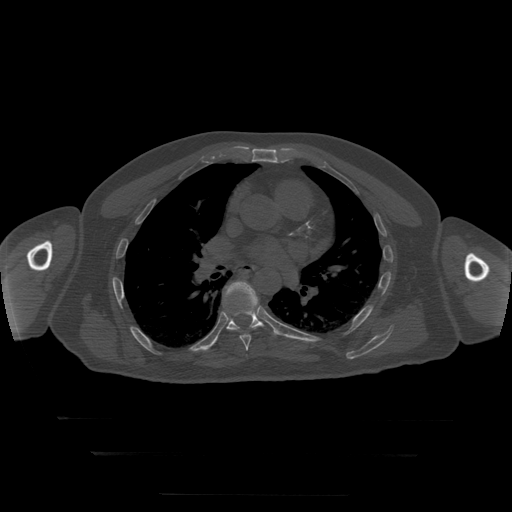
CT including the spine, one axial slice; position 177 of 397 along the scan axis; reconstruction kernel STANDARD; bone window (W 1800 / L 400 HU); 1.25 mm slice thickness; 512 × 512 image matrix. Patient age 73 years. Case-level facts recorded for this patient, not image findings: primary cancer: prostate.
Outlined on this slice (semi-automatically segmented with operator editing):
- T7 vertebra: box from (x=229, y=330) to (x=251, y=351) px
- T8 vertebra: (x=212, y=282)–(x=277, y=346)